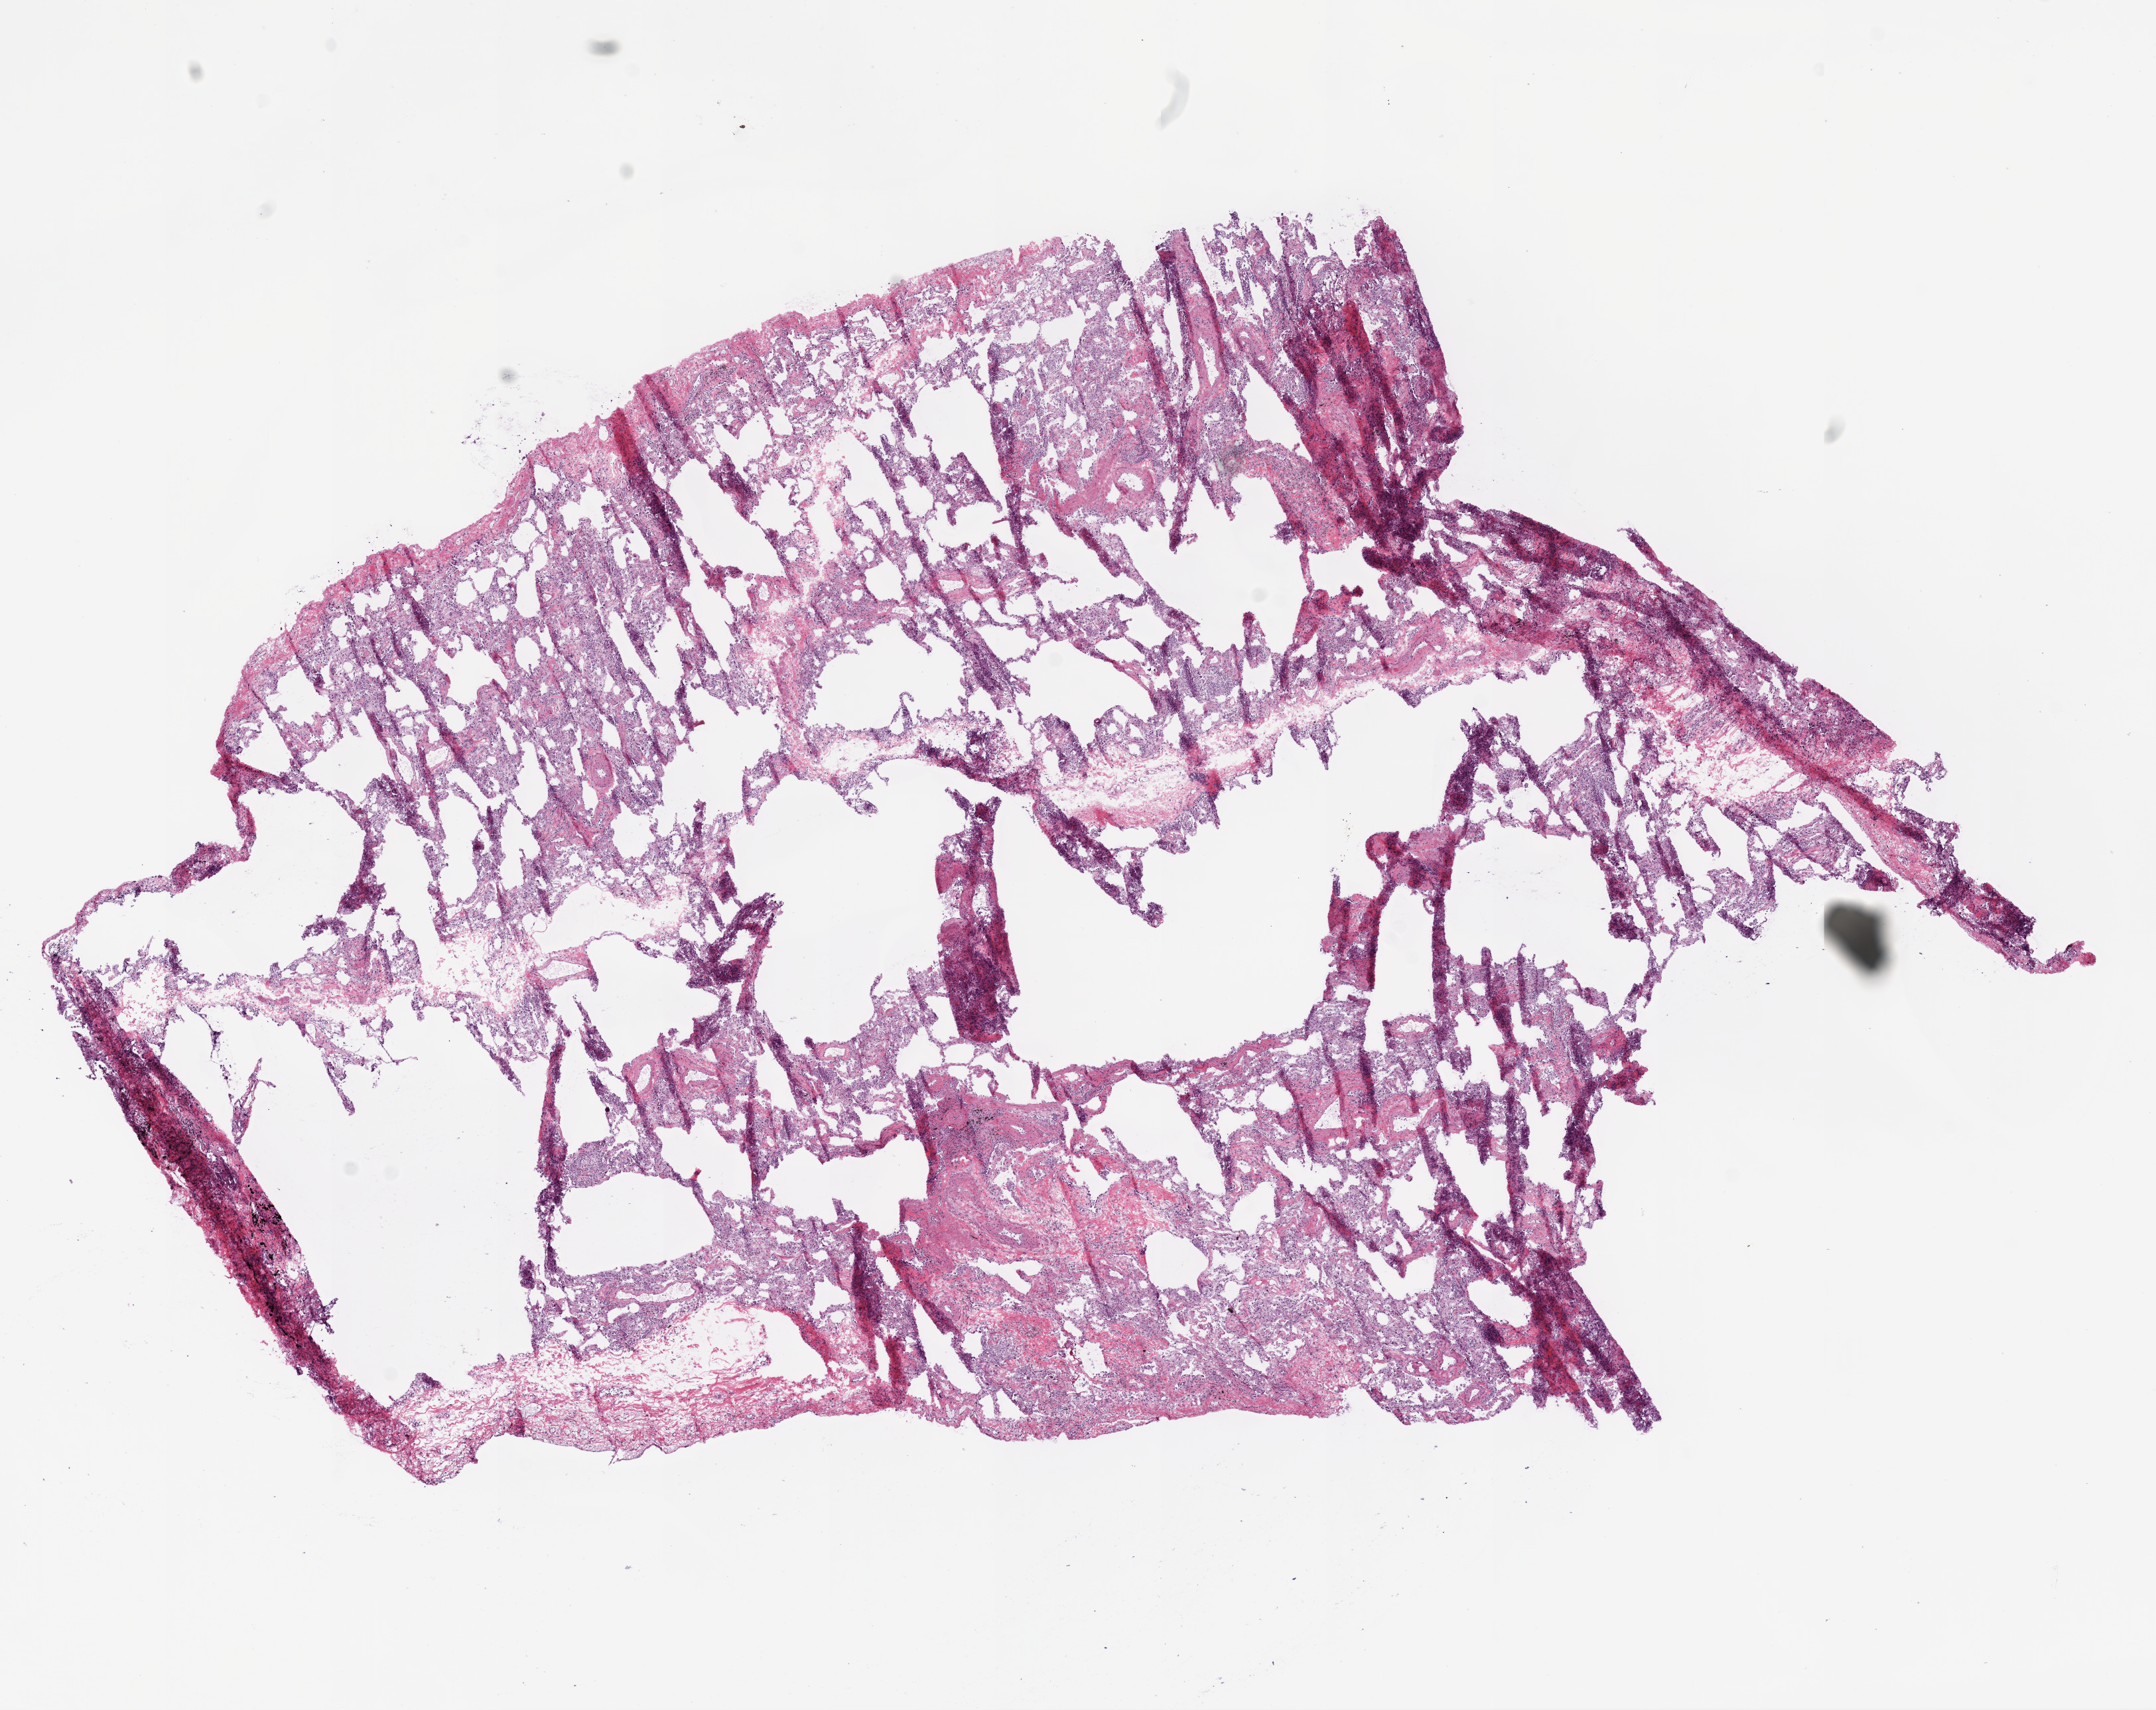
H&E whole-slide image — a low-resolution overview of the entire scanned area, about 13.0 x 10.3 mm, frozen section from the bottom of the tissue portion, solid tissue normal (non-tumour tissue) sample from the lung. Male, age 71 years at initial diagnosis.
• this section: solid tissue normal (non-tumour) sample from the same patient
• patient diagnosis: Squamous cell carcinoma, NOS (upper lobe, lung)